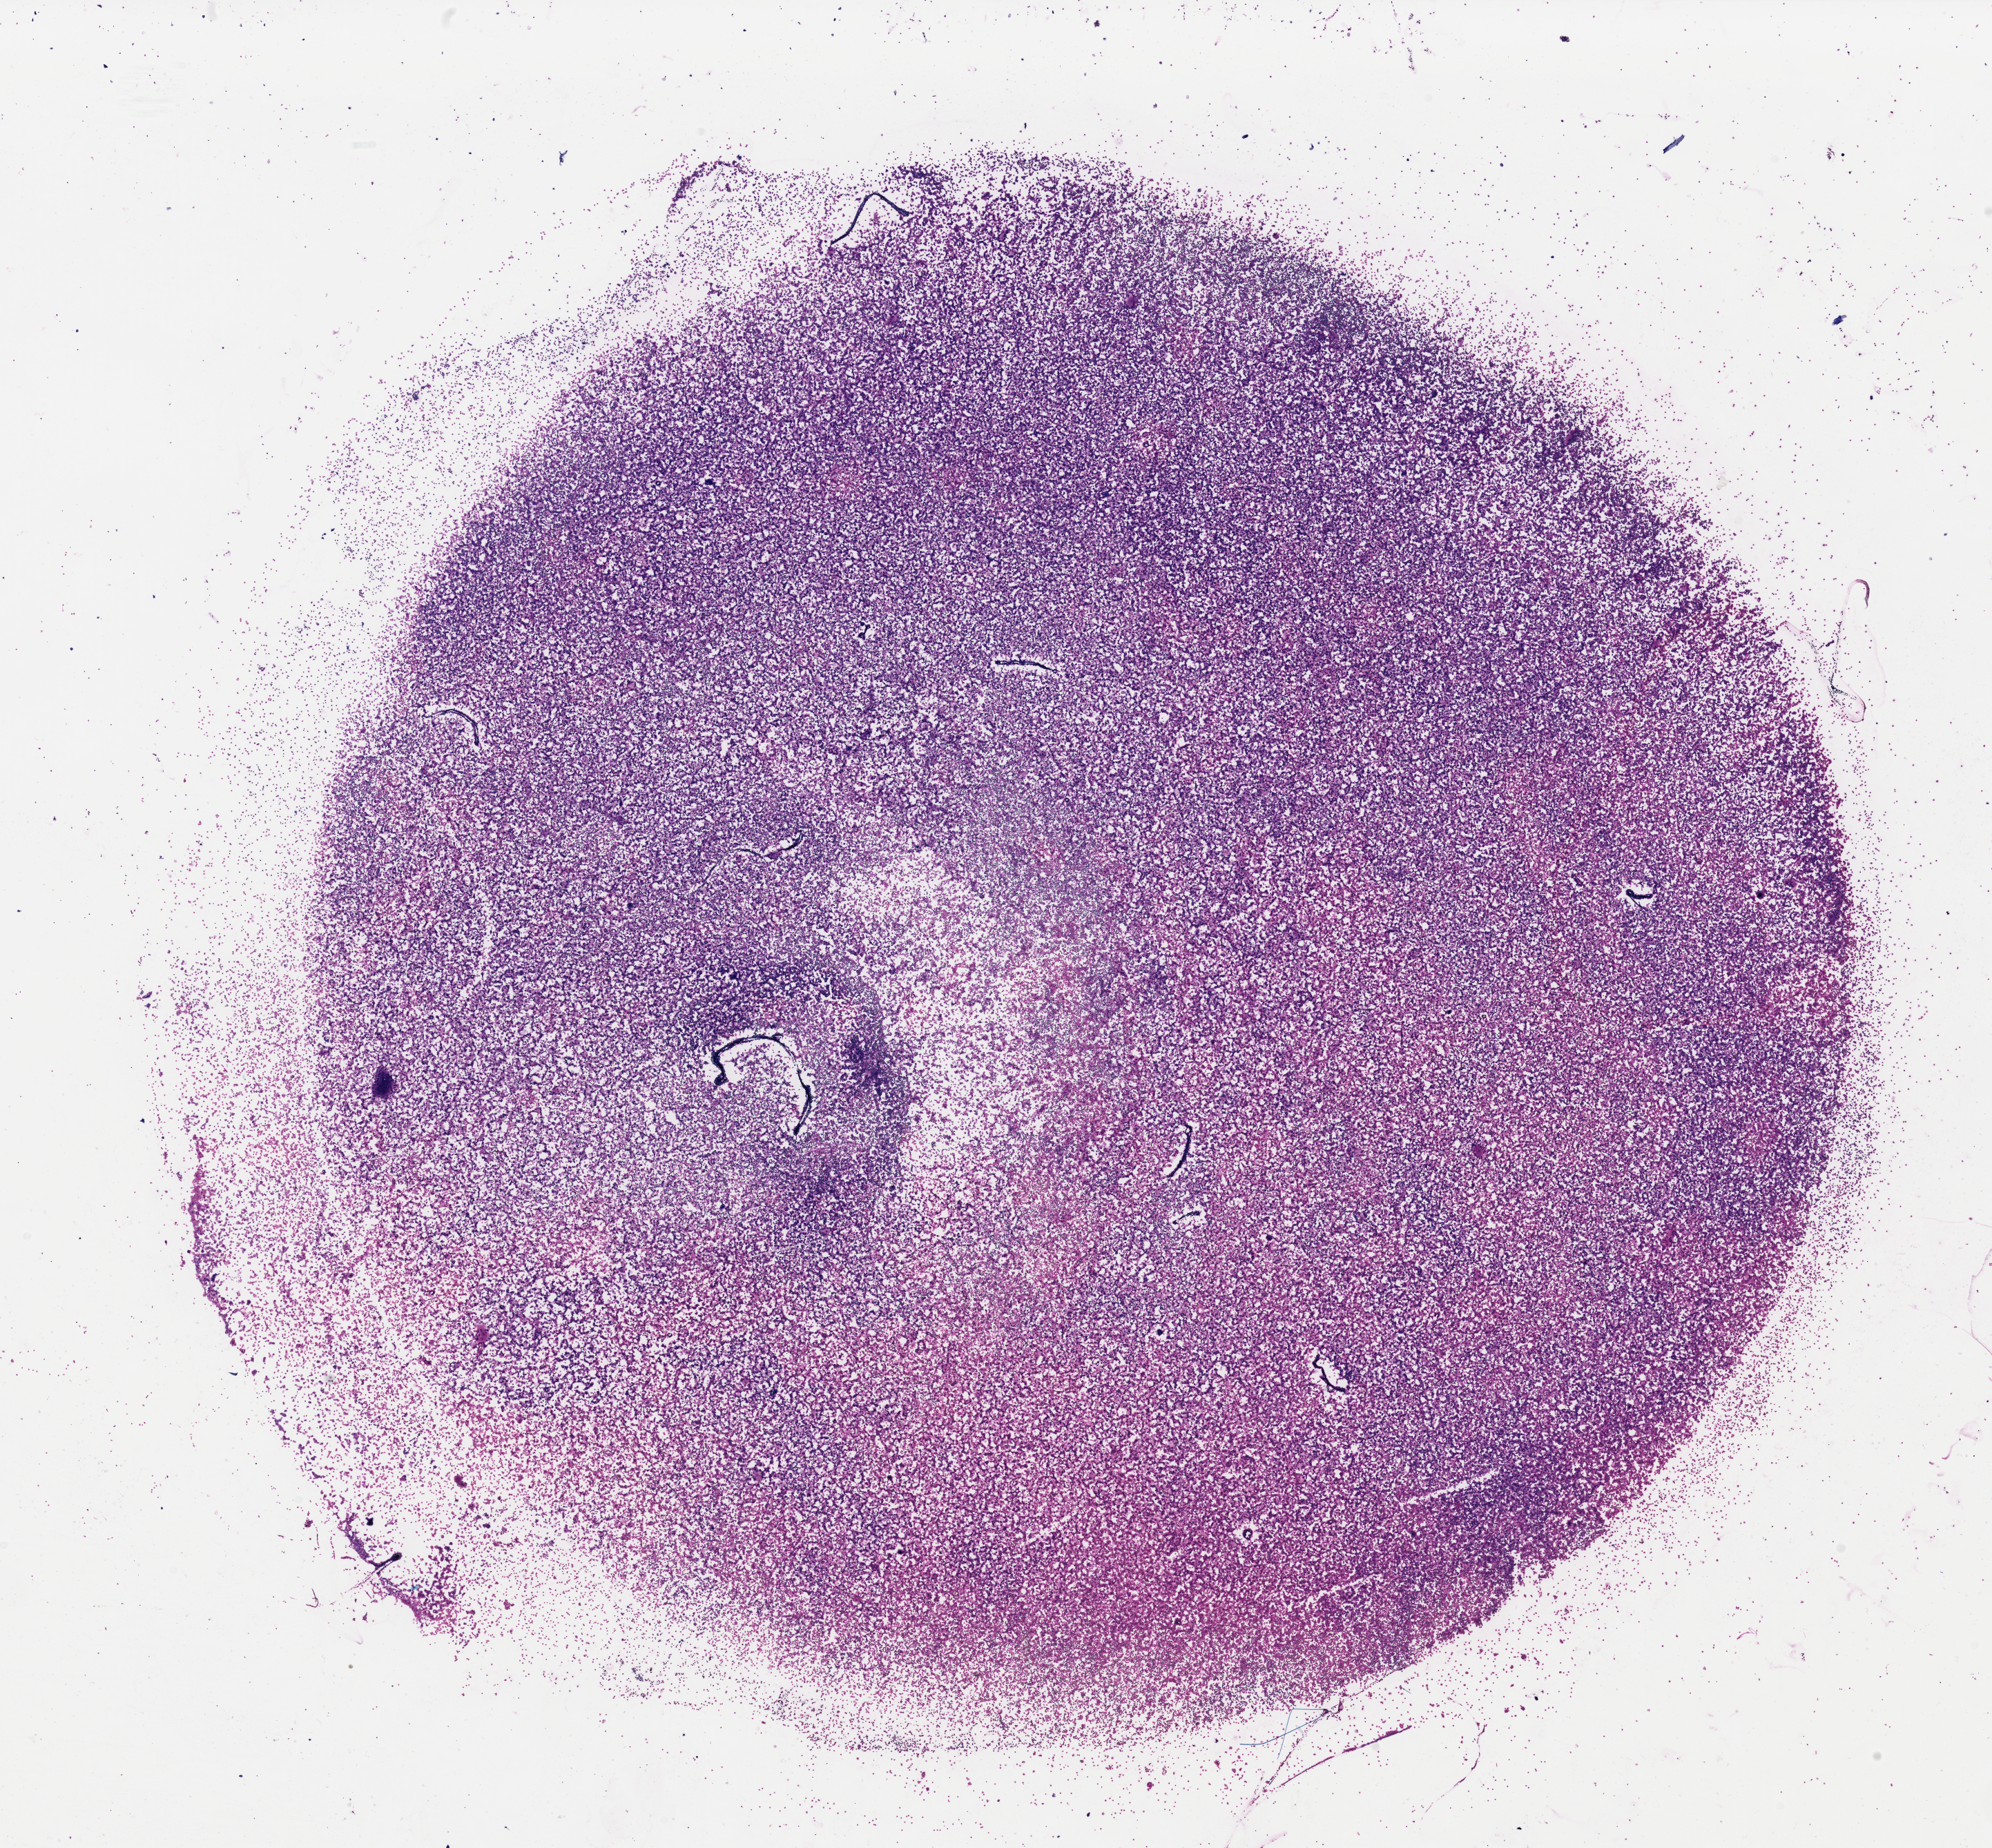
Digitized H&E tissue section (whole slide), low-resolution overview of the scanned area, about 22.8 x 21.1 mm. Bone marrow (leukaemic) sample. Male, 38 y/o. Blasts: 95%.
- FAB classification: M1
- diagnosis: Acute Myeloid Leukemia